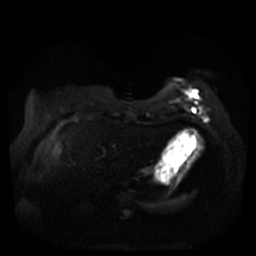
Breast MRI, one axial slice; slice 7 of 44 in the series (ordered by position); diffusion-weighted series; image 2 of 4 stored at this slice position (different b-values; order by instance number); 3 T; 5 mm slice thickness; 256 × 256 image matrix, field of view 360 × 360 mm. Female patient.
Outlined on this slice (expert manual segmentation):
- tumour on diffusion-weighted imaging: bounding box (x1, y1, x2, y2) in pixels: (189, 90, 195, 98)